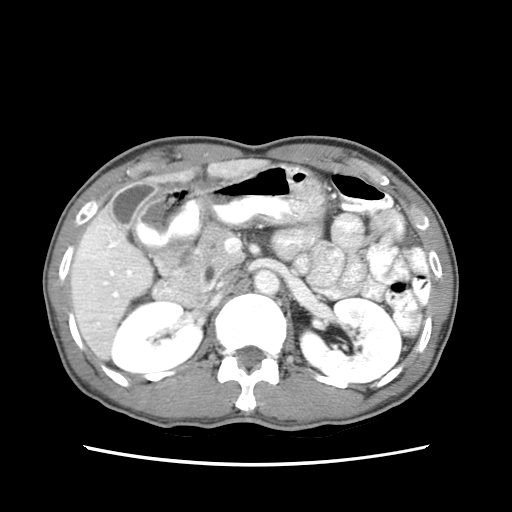
Contrast-enhanced abdominal CT (liver protocol), one axial slice; slice 29 of 79 in the series (ordered by position); reconstruction kernel STANDARD; soft-tissue window (W 400 / L 40 HU); 512 × 512 image matrix, field of view 320 × 320 mm. Case-level facts recorded for this patient, not image findings: diagnosis: hepatocellular carcinoma (patient treated with transarterial chemoembolisation; whether this scan precedes or follows treatment is not stated here); TNM stage (as recorded): Stage-IIIB; Child-Pugh class: A; tumour nodularity: multinodular.
Outlined on this slice (semi-automatic segmentation, software-assisted and operator-edited):
- liver parenchyma outside the tumour (the mass and vessels are separate outlines, so this box may not span the whole liver): box from (x=70, y=158) to (x=263, y=358) px
- liver vessels: (x=83, y=222)–(x=146, y=325)